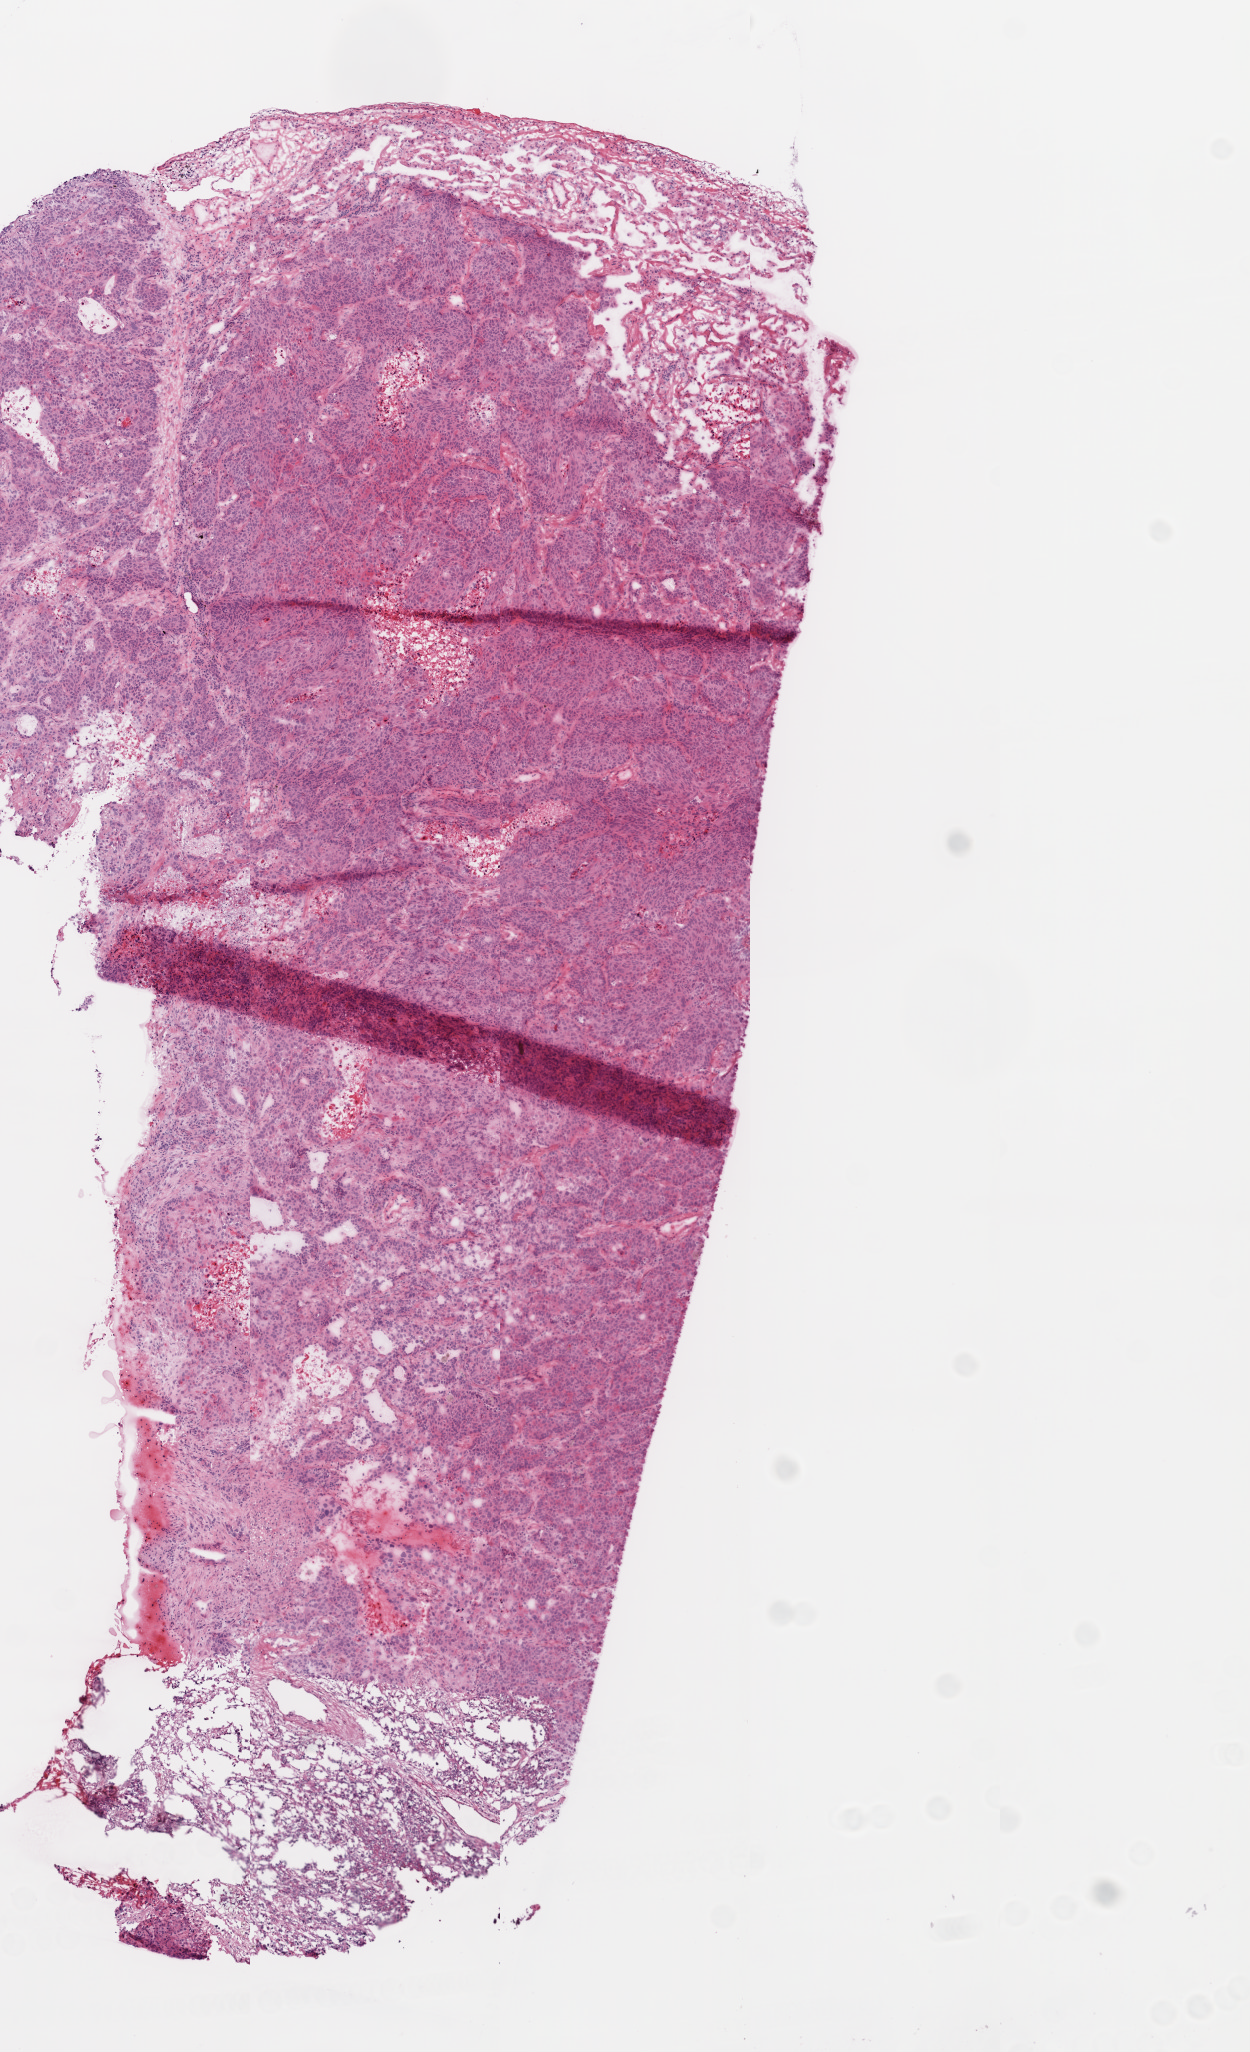
H&E-stained whole-slide image — whole scanned area (about 5.0 x 8.2 mm, slide scanned at 20x) shown as a low-resolution overview; frozen section from the top of the tissue portion; sample: primary tumour, lung. Patient: female, age at initial diagnosis 73 years. Slide review estimates, as recorded: tumour cells 75%, tumour nuclei 80%, normal cells 15%, stromal cells 5%, necrosis 5%.
TNM: T4 N0 M0. Diagnosis: Squamous cell carcinoma, NOS (upper lobe, lung). AJCC pathologic stage: IIIA.